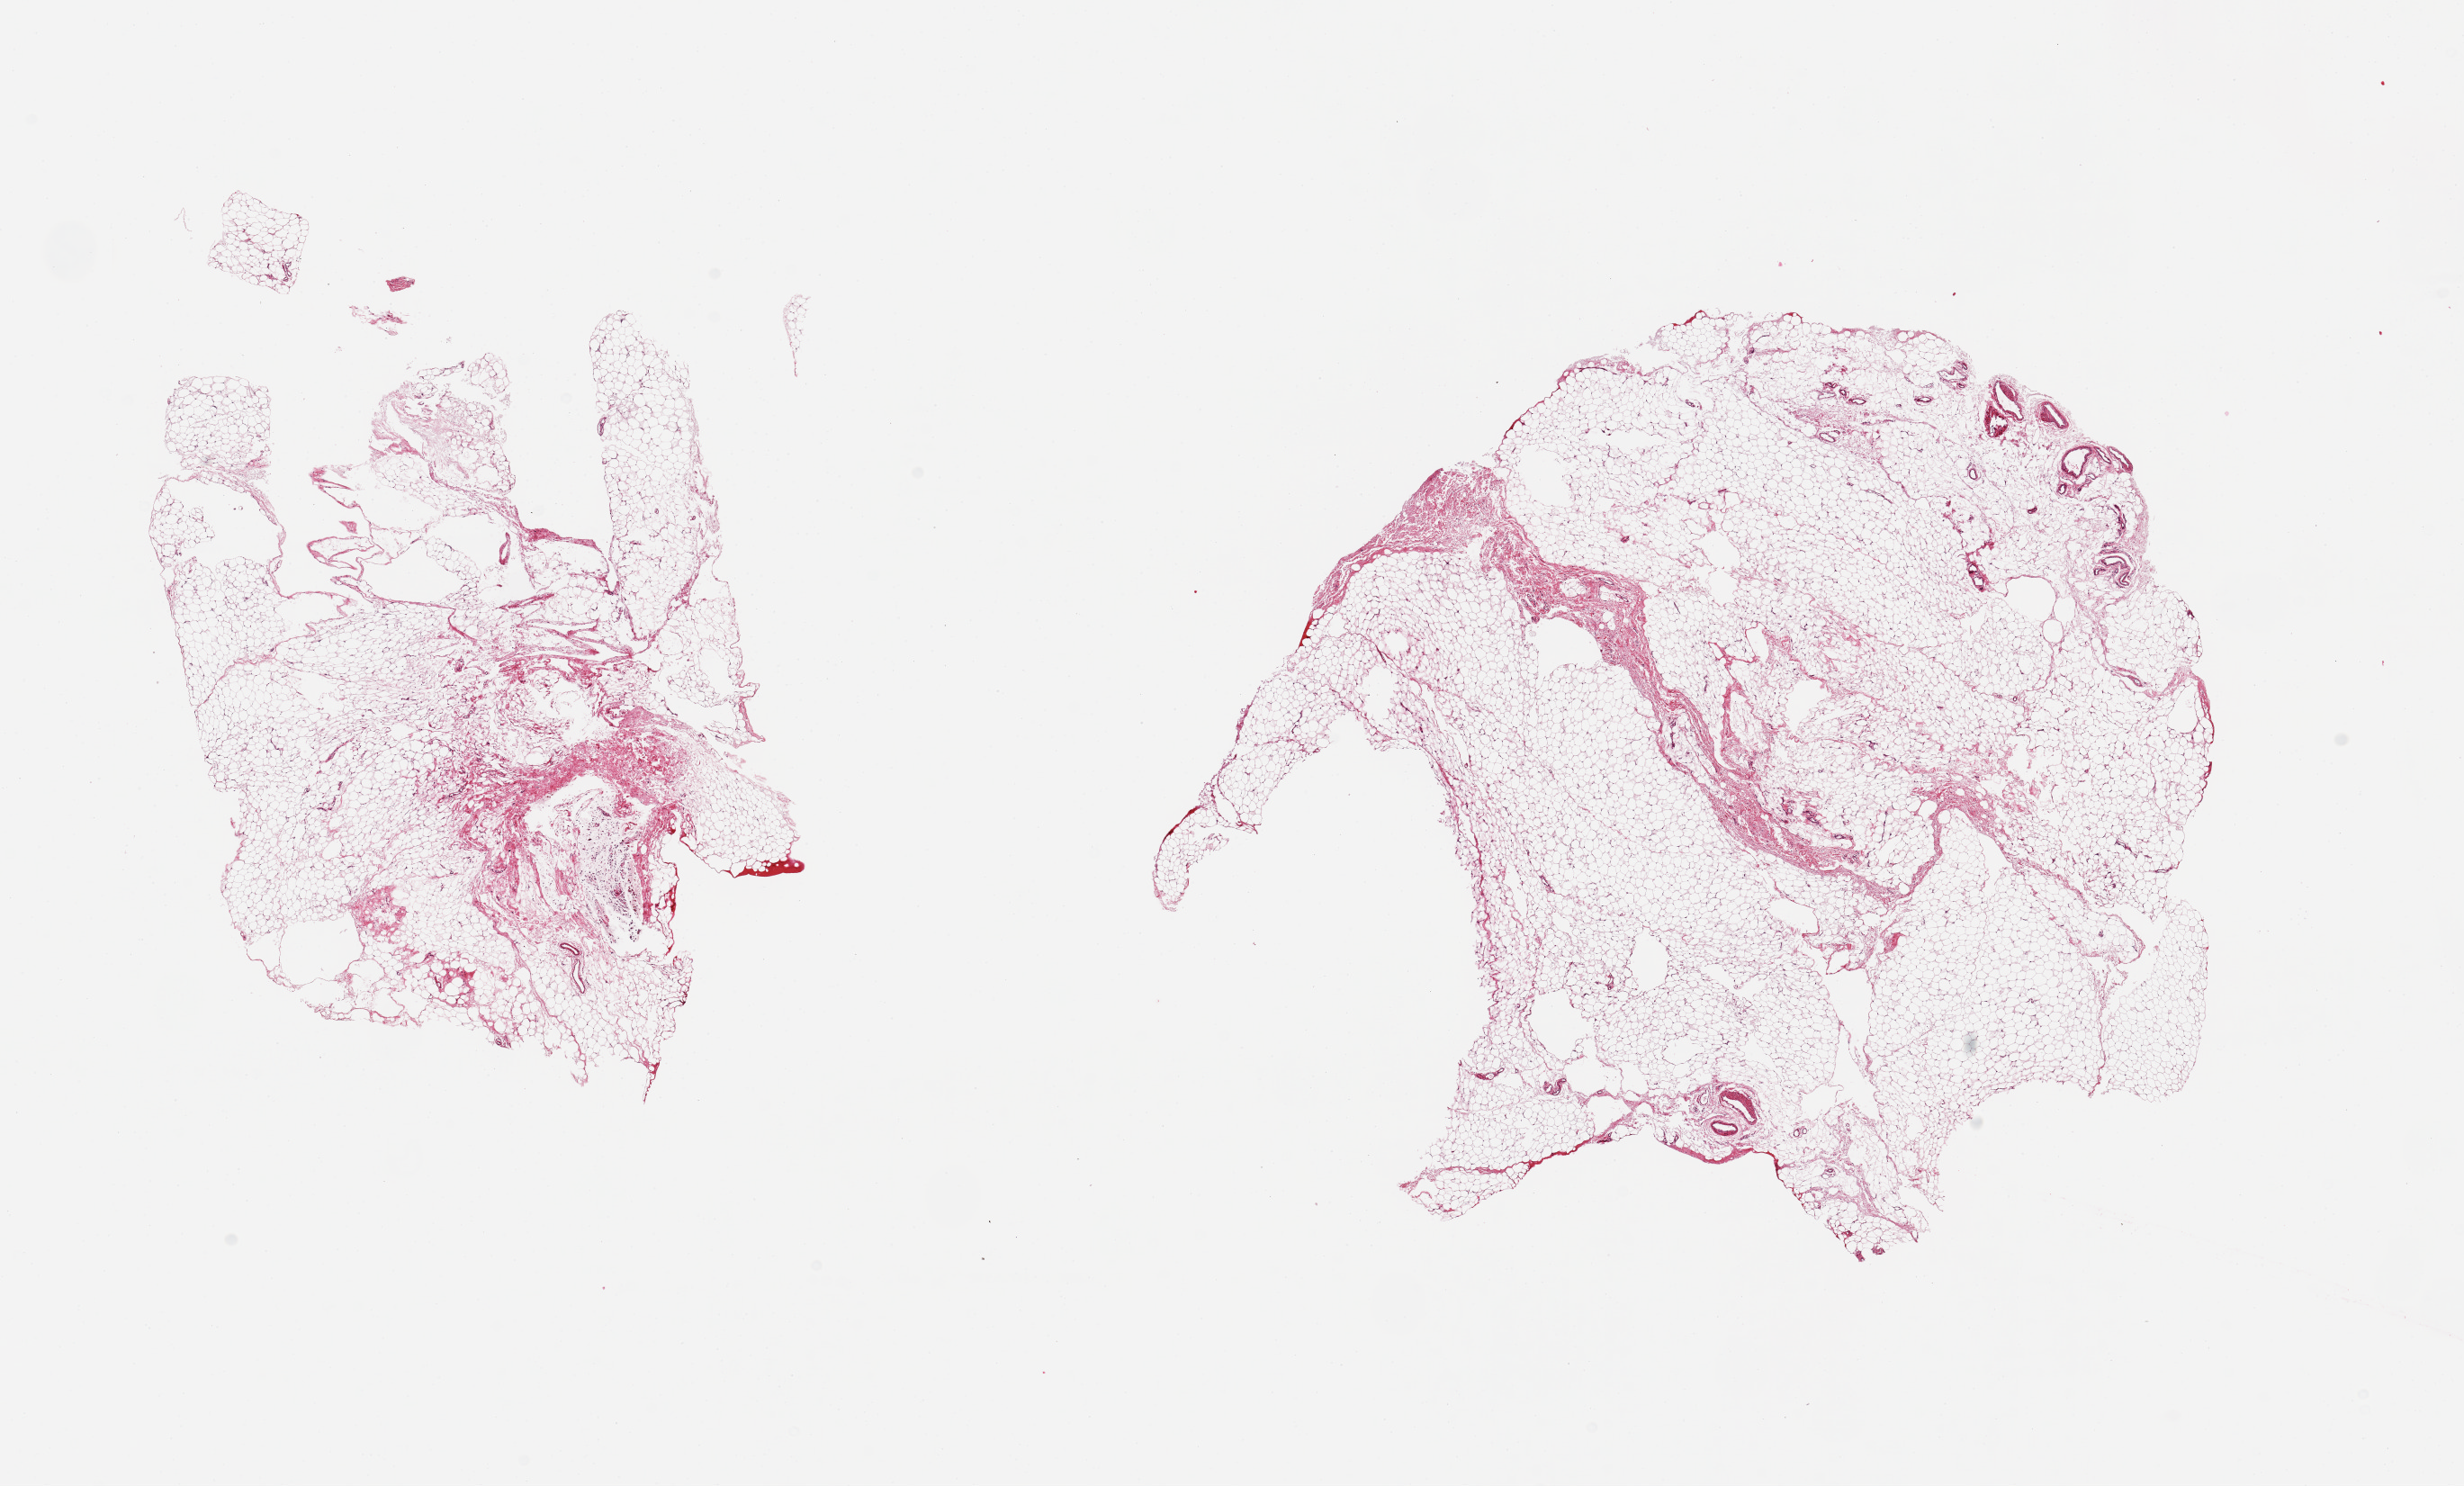
Digitized hematoxylin and eosin (H&E)-stained section — shown as a low-resolution overview of the whole scanned area (about 21.7 x 13.1 mm, acquisition: 20x scan), PAXgene-fixed paraffin-embedded (PFPE) section, sampled site (target tissue): omentum, tissue donor sample.
Reviewer comment on this tissue sample: 2 pieces; 5% fibrous content.